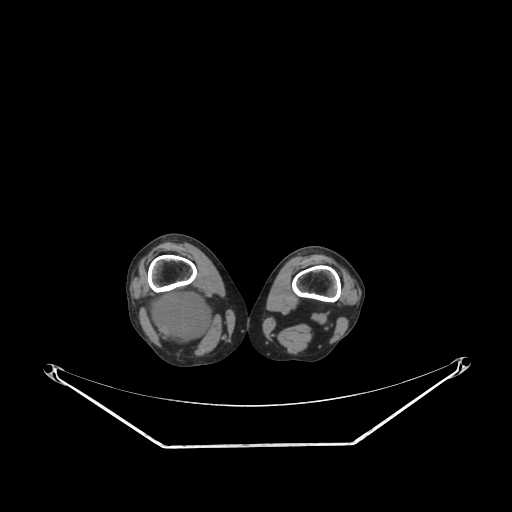
CT of an extremity soft-tissue mass (from a PET/CT study), one axial slice; slice 182 of 267 in the series (ordered by position); 140 kVp; soft-tissue window (W 400 / L 40 HU); 3.75 mm slice thickness; 512 × 512 image matrix. Female patient. Case-level facts recorded for this patient, not image findings: histological type: liposarcoma; site of the primary tumour: right thigh.
Structures marked on this image (expert contour drawn on MRI and transferred to this co-registered scan by the dataset authors):
- gross tumour volume (mass): bounding box <144,290,215,350> (left, top, right, bottom; pixels)